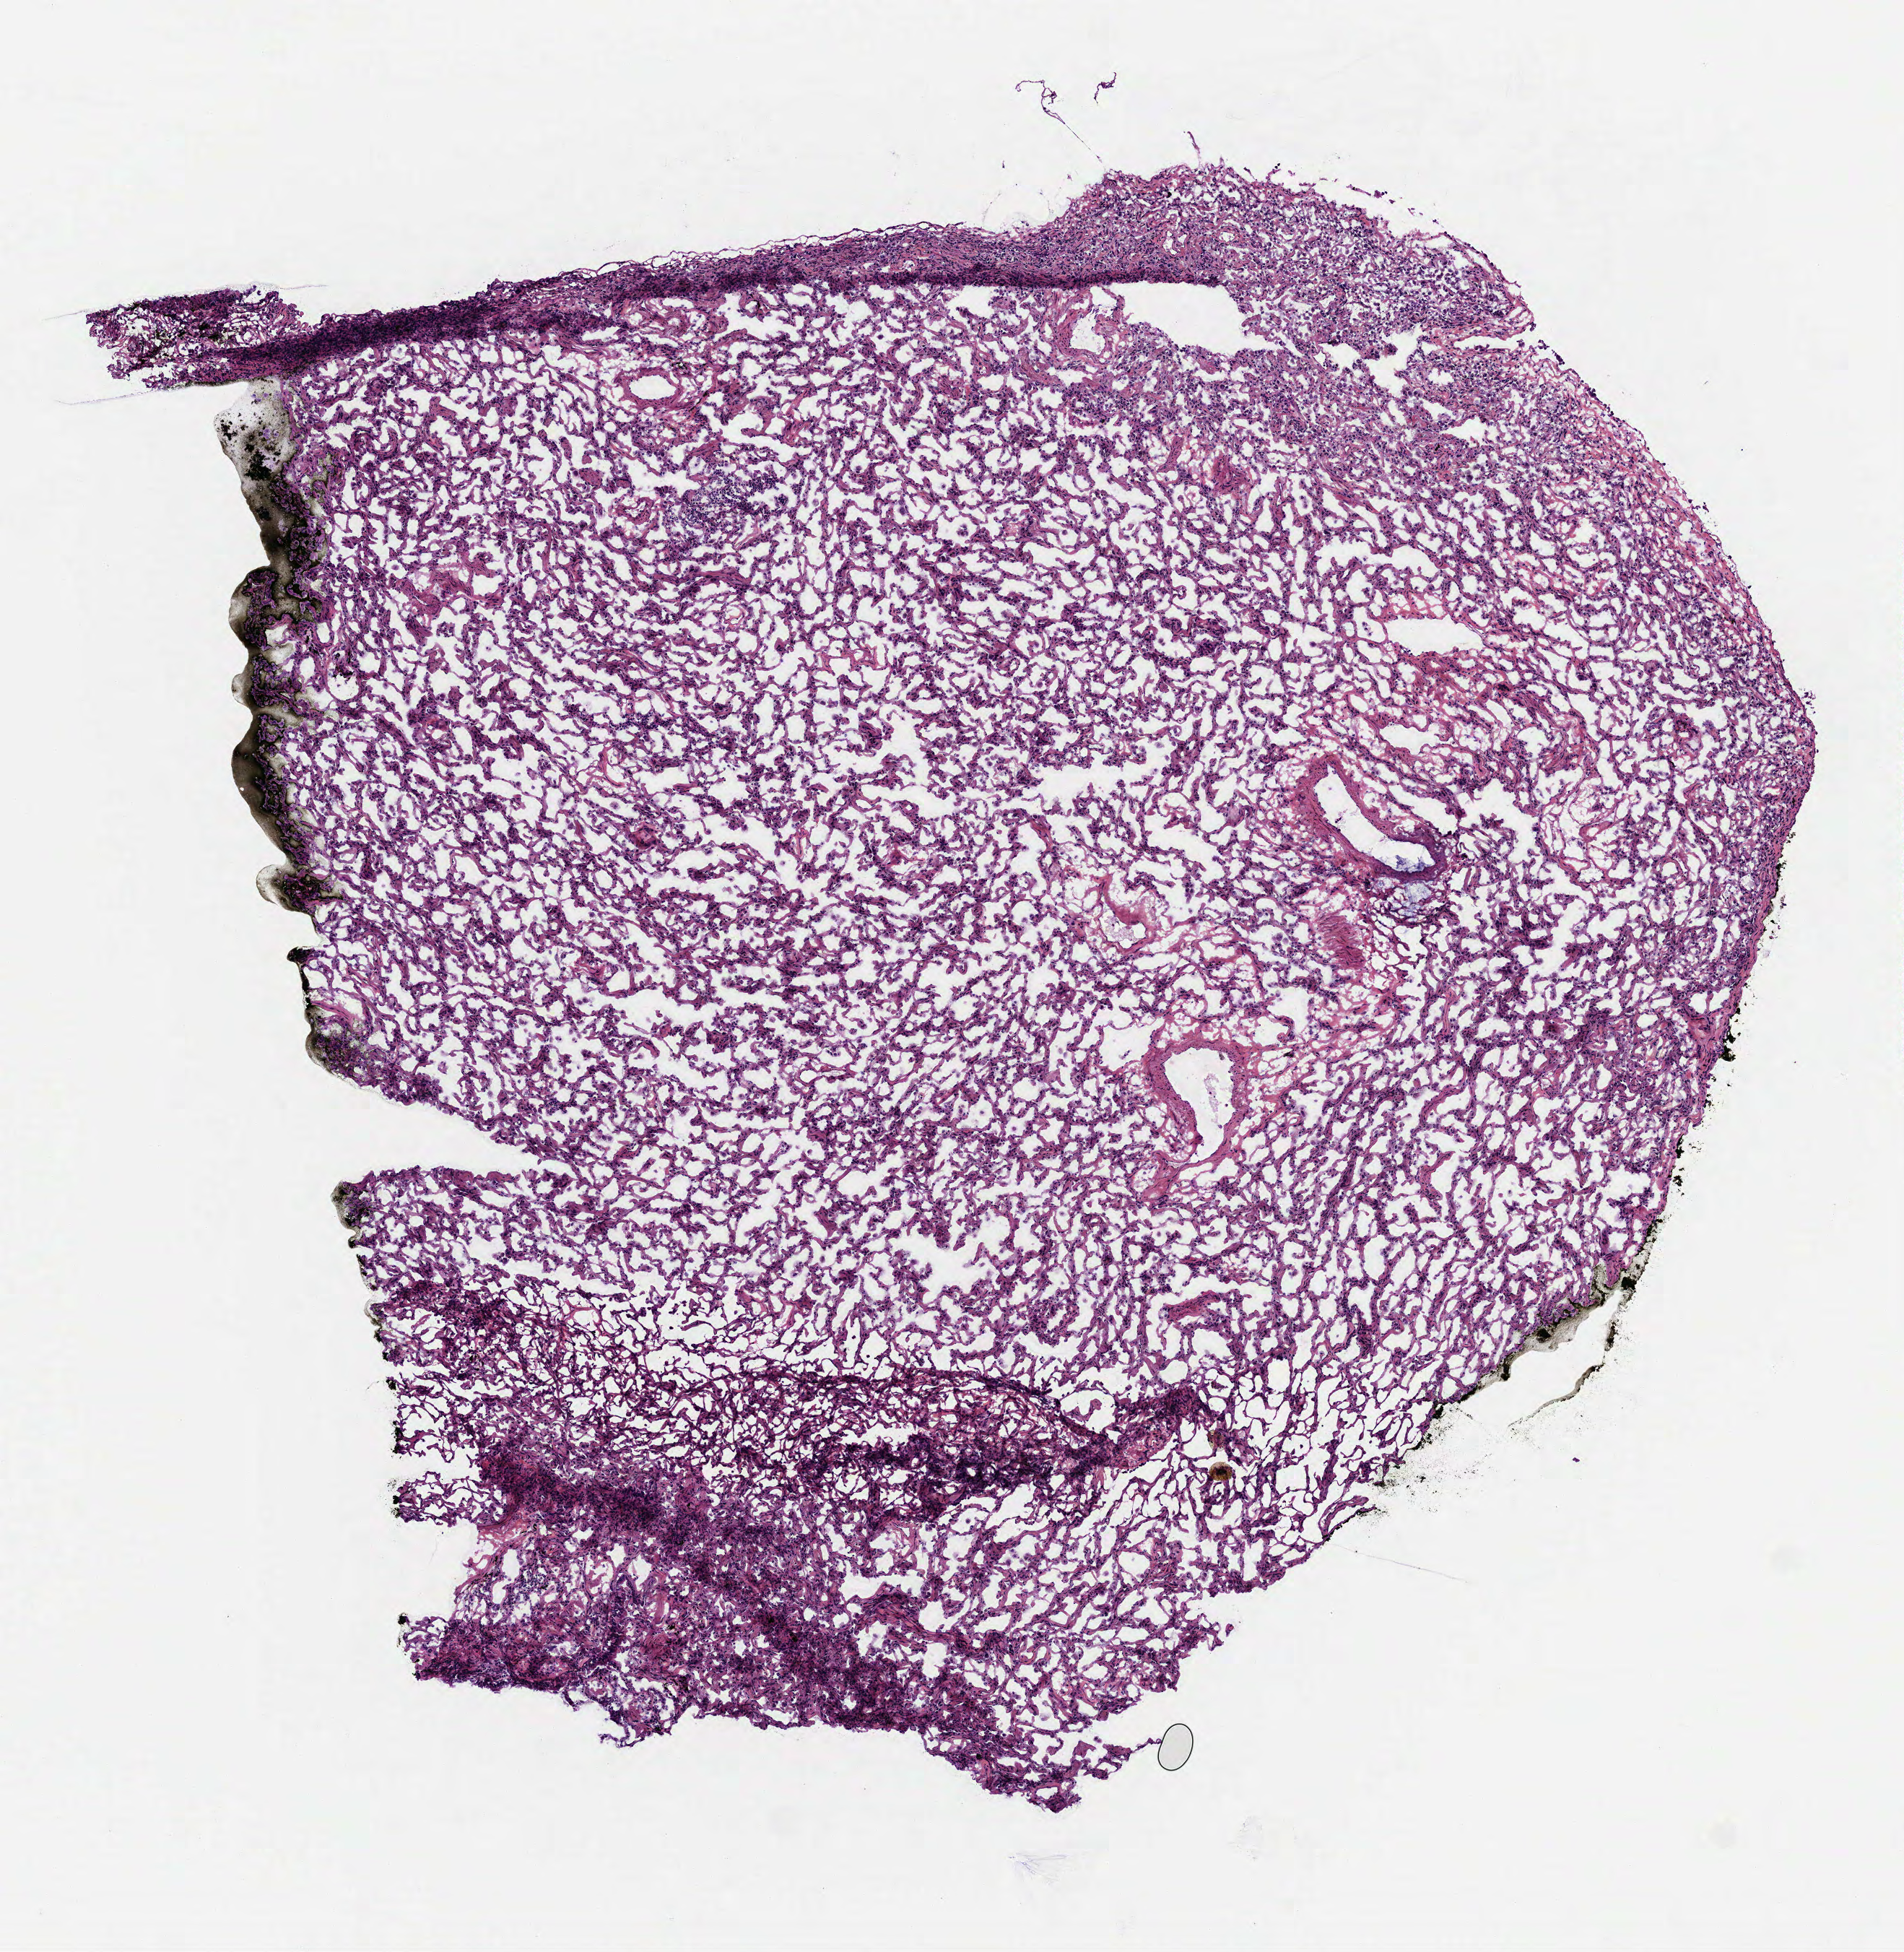
Whole-slide histology image, Hematoxylin and eosin (H&E) stained — shown as a low-resolution overview of the whole scanned area (about 5.3 x 5.5 mm, acquisition: 40x scan); frozen section from the top of the tissue portion; lung, solid tissue normal (non-tumour tissue) sample. Patient: female, age at initial diagnosis 62 years. Inflammatory infiltration, as recorded: lymphocyte infiltration 2%, monocyte infiltration 14%, neutrophil infiltration 0%.
• this section: solid tissue normal (non-tumour) sample from the same patient
• patient diagnosis: Squamous cell carcinoma, keratinizing, NOS